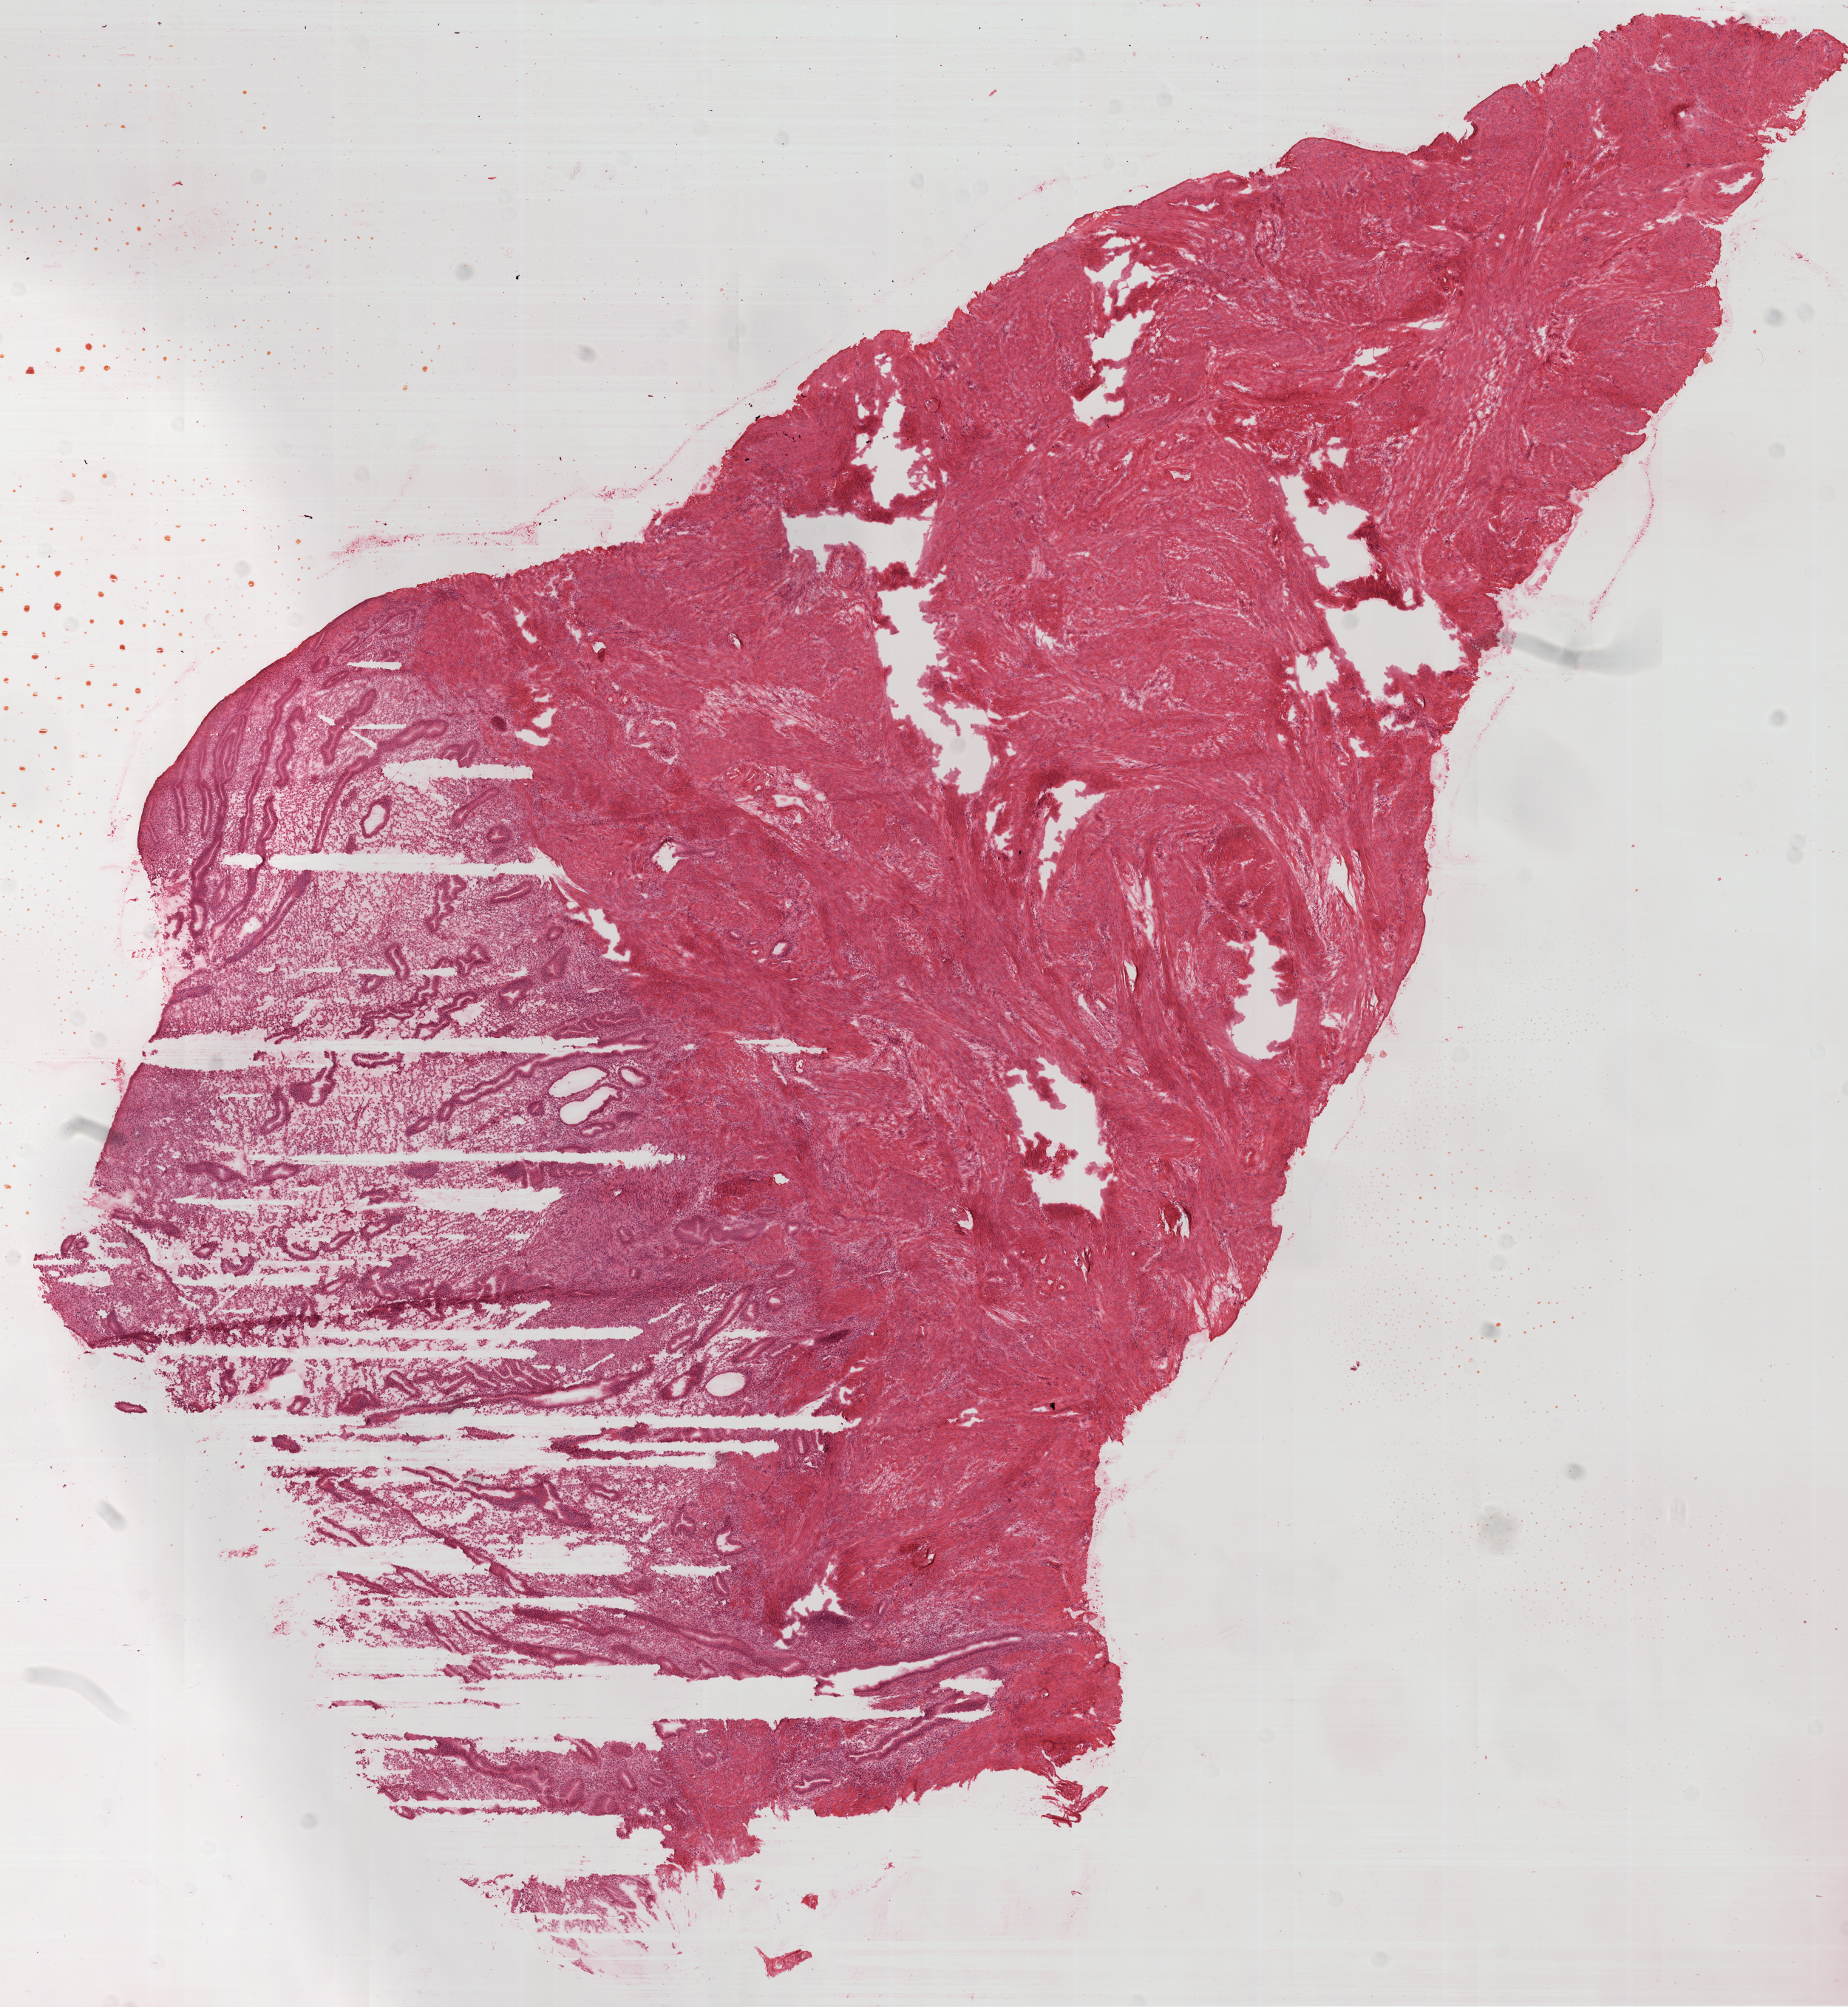
Digitized H&E tissue section (whole slide), whole scanned area (about 10.0 x 10.9 mm, acquisition: 20x scan) shown as a low-resolution overview. Frozen section. Sample: solid tissue normal (non-tumour tissue), ovary. Female patient; age at initial diagnosis 45 years.
* this section: solid tissue normal (non-tumour) sample from the same patient
* patient diagnosis: Serous cystadenocarcinoma, NOS